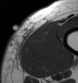
MRI of an extremity soft-tissue mass, one axial slice; slice 8 of 43 in the series (ordered by position); MR volume resampled by the dataset authors to the PET/CT grid (not the native acquisition matrix); 3.27 mm slice thickness; 78 × 83 image matrix. Male patient. Case-level facts recorded for this patient, not image findings: histological type: pleiomorphic leiomyosarcoma; grade: high; site of the primary tumour: left thigh.
Annotated regions visible in this slice (expert contour drawn on MRI and transferred to this co-registered scan by the dataset authors):
- gross tumour volume including surrounding oedema: bounding box [x1, y1, x2, y2] px = [20, 21, 57, 73]